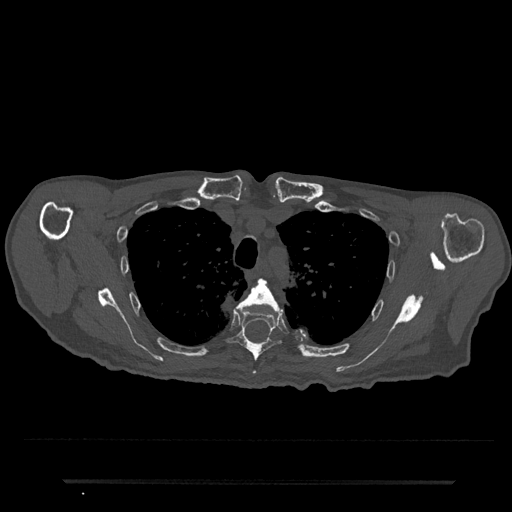
CT including the spine, one axial slice; position 588 of 797 along the scan axis; reconstruction kernel Br40s/3; 120 kVp; bone window (W 1800 / L 400 HU); 0.5 mm slice thickness; 512 × 512 image matrix, field of view 427 × 427 mm. Male patient, age 74 years. From the clinical record (not read from this slice): primary cancer: prostate.
Structures marked on this image (semi-automatically segmented with operator editing):
- T4 vertebra: bounding box [x1, y1, x2, y2] px = [243, 279, 283, 373]
- T5 vertebra: [228, 301, 282, 362]